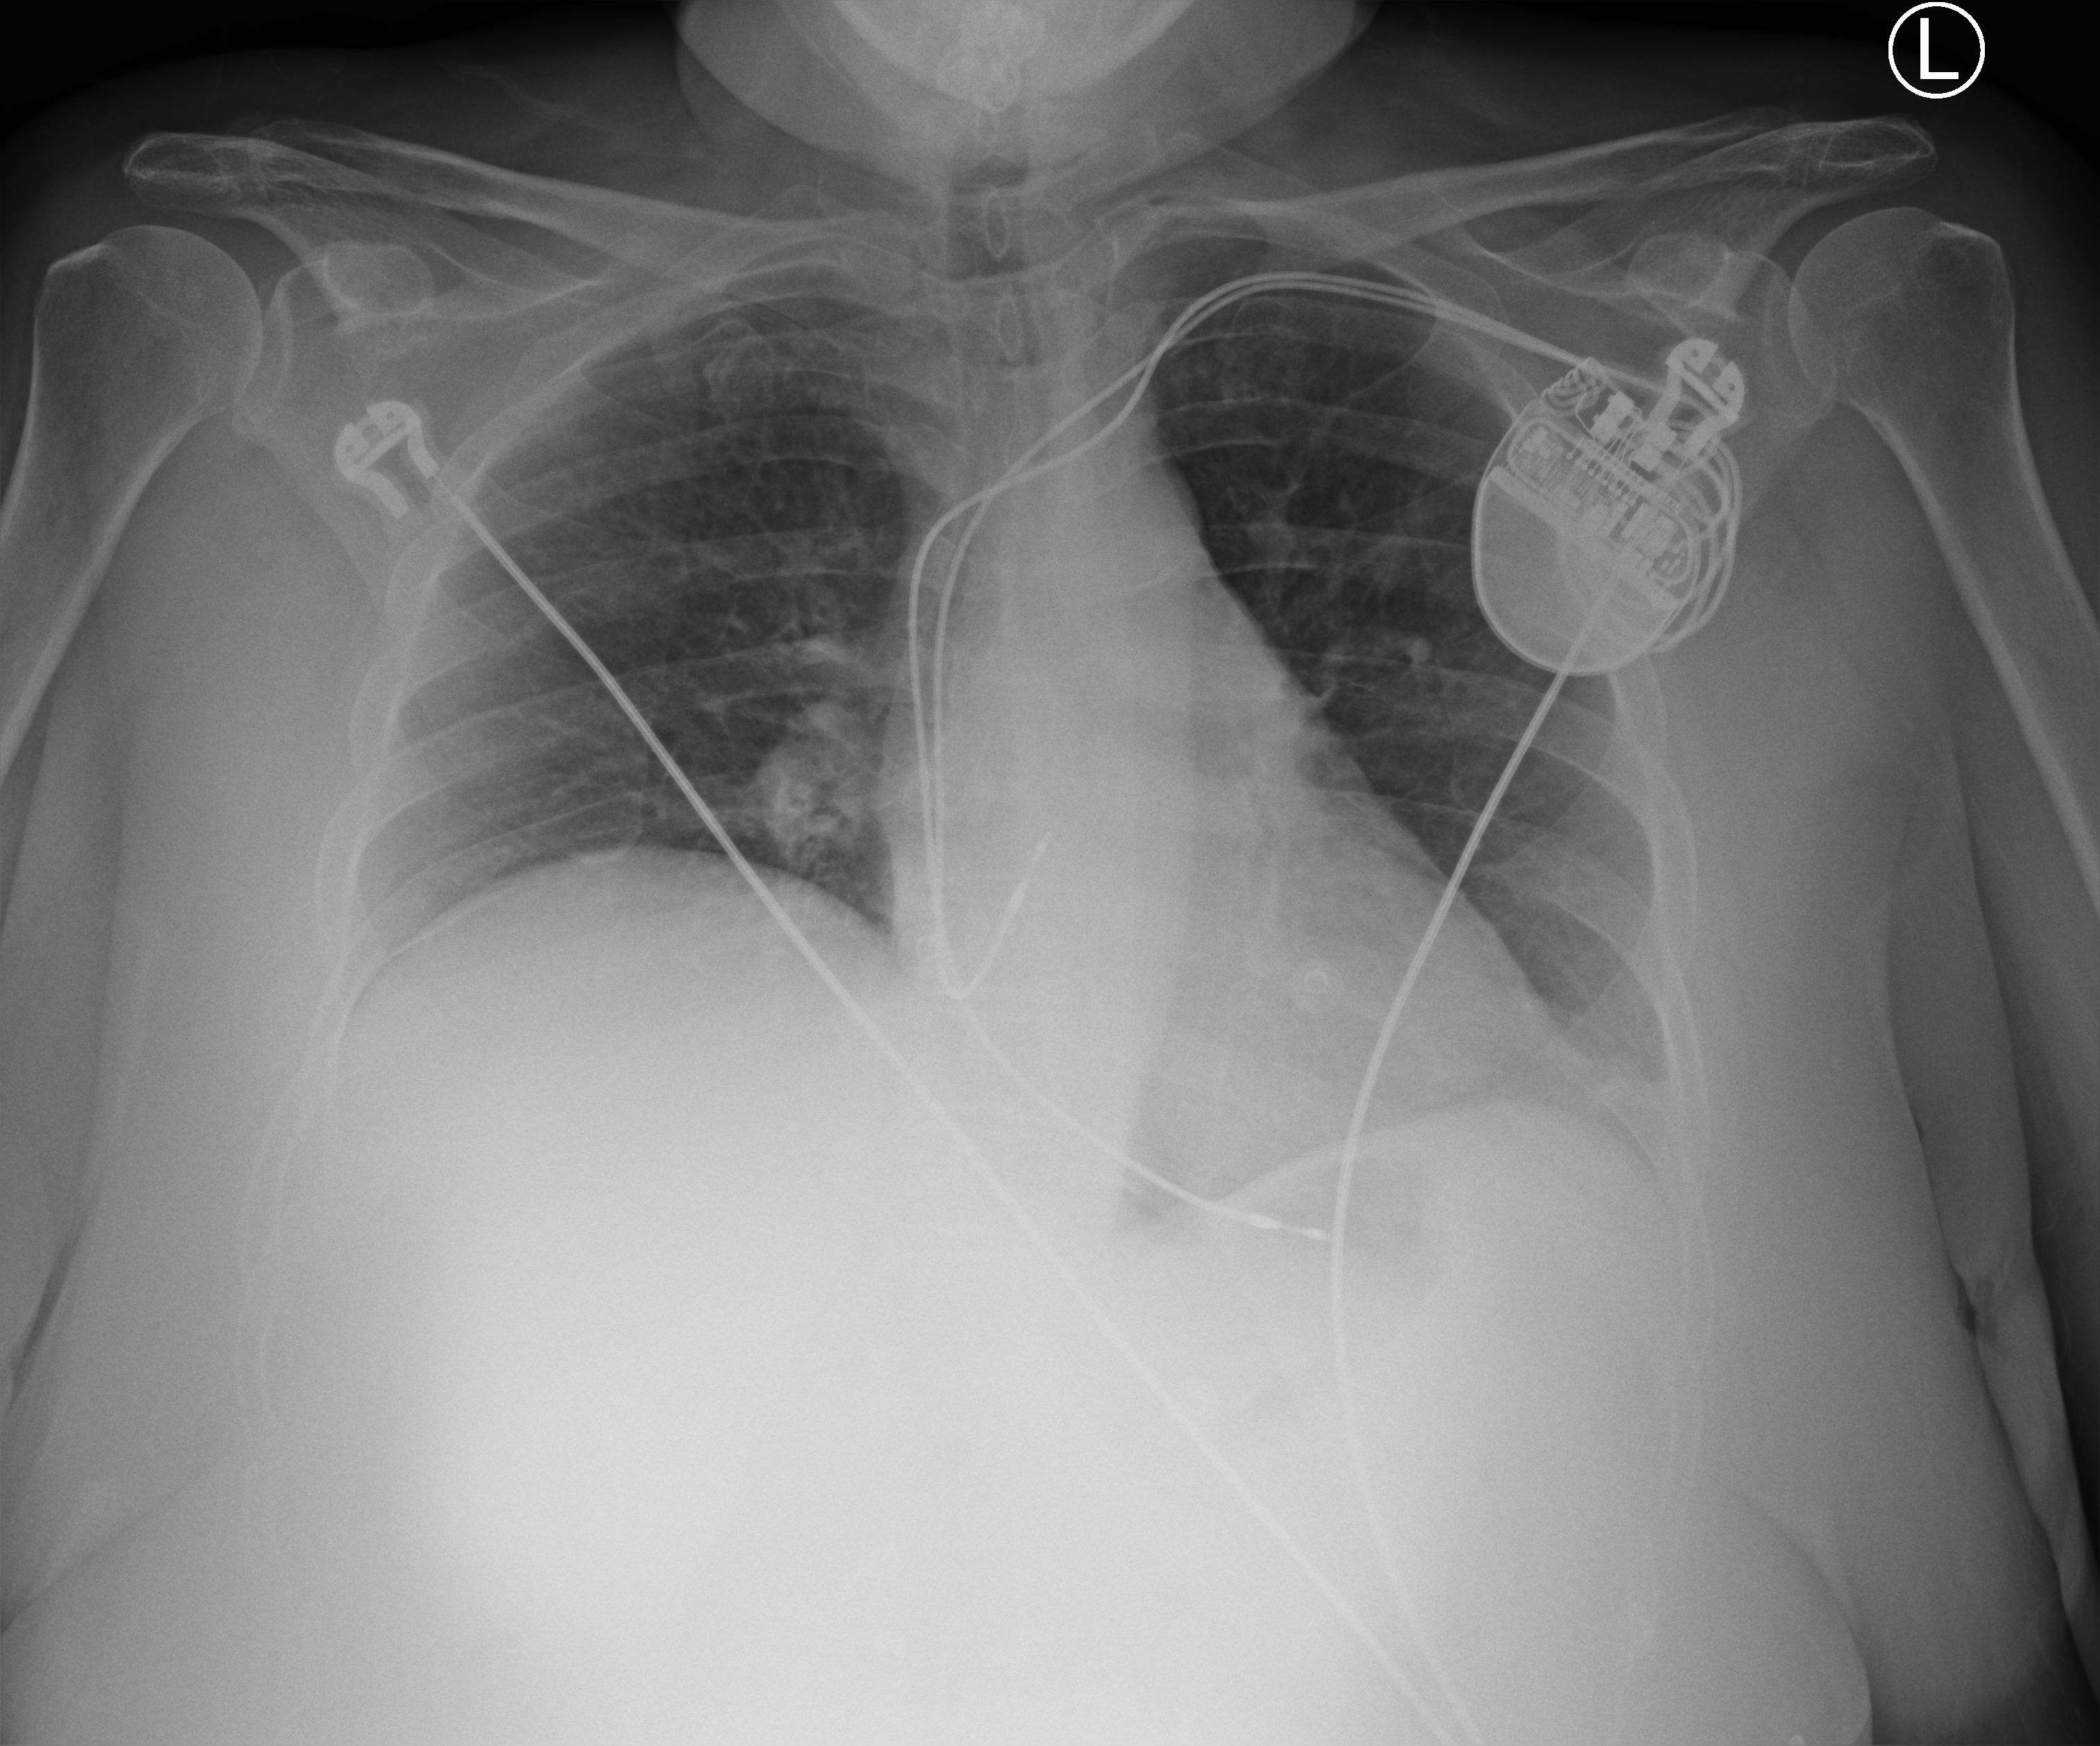
Portable chest radiograph. Patient hospitalised with COVID-19; female, aged 18–59 years.
Admission-level facts for this patient (not findings on this image; timing relative to this image not recorded):
- mechanically ventilated during this hospital stay: no
- admitted to intensive care during this hospital stay: no